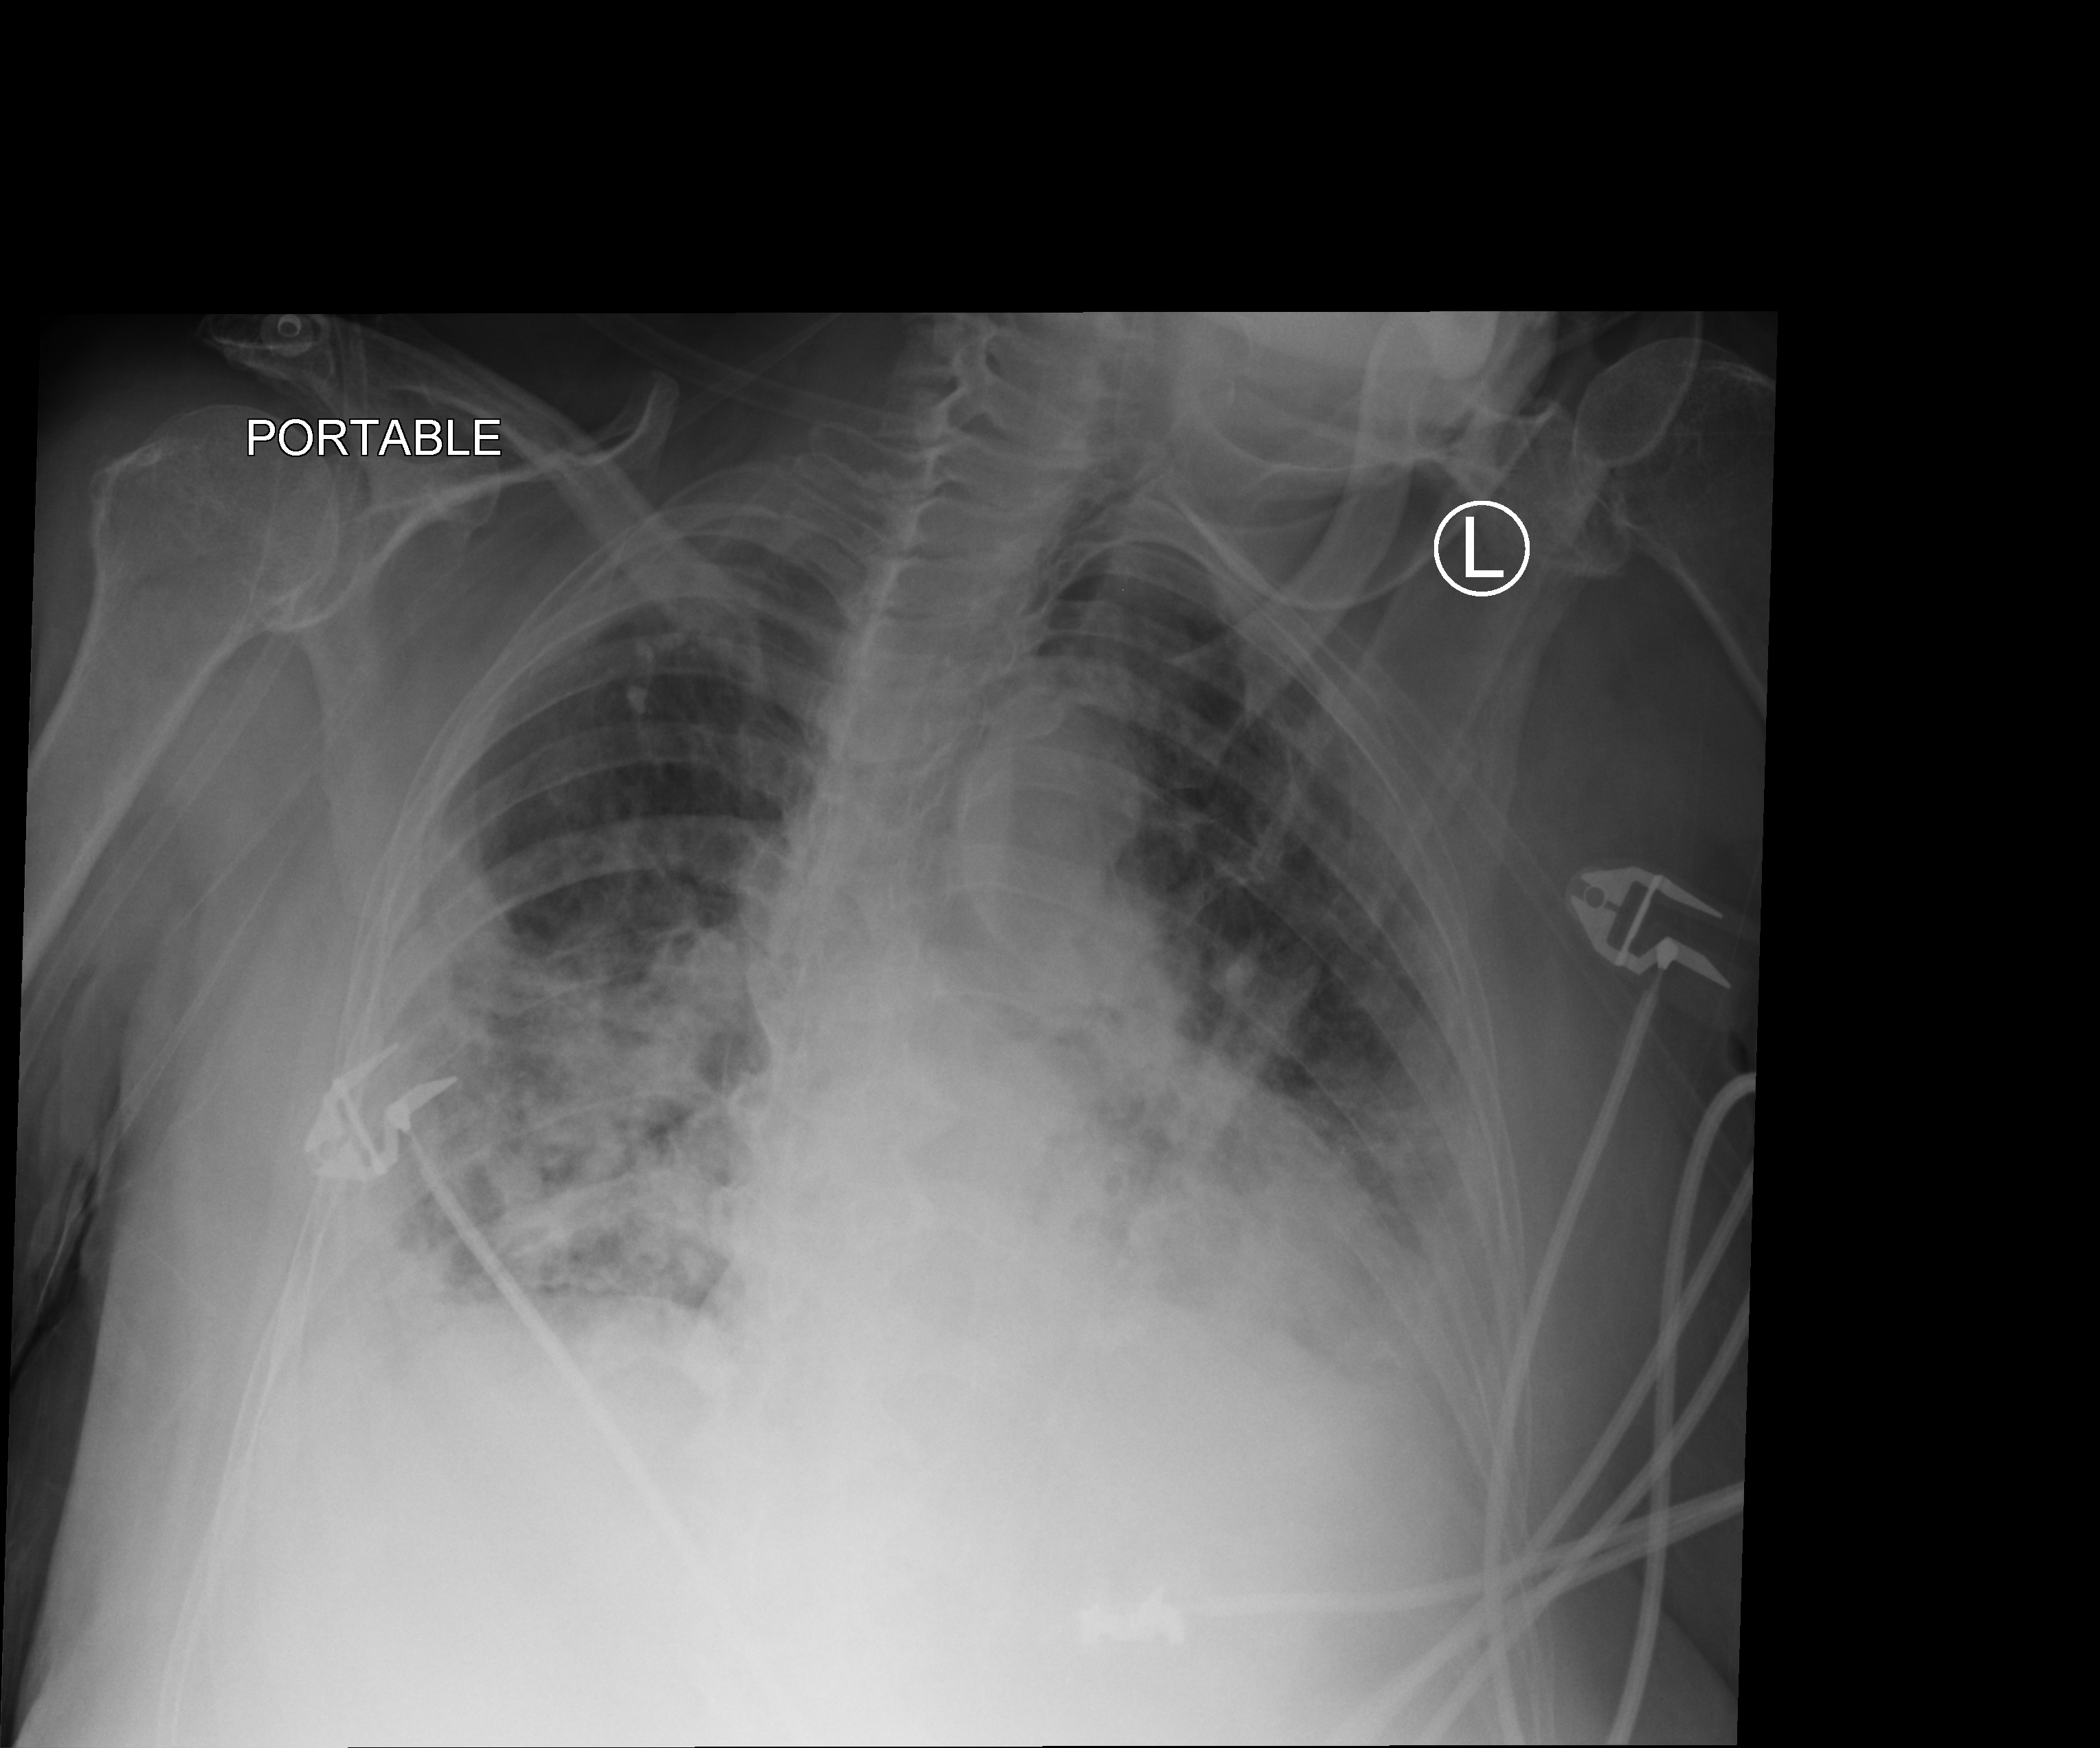
Bedside chest radiograph (computed radiography); anteroposterior (AP) projection. Patient hospitalised with COVID-19; female, aged 75–90 years.
Admission-level facts for this patient (not findings on this image; timing relative to this image not recorded): mechanically ventilated during this hospital stay: no; admitted to intensive care during this hospital stay: yes; chronic kidney disease (admission record): no.